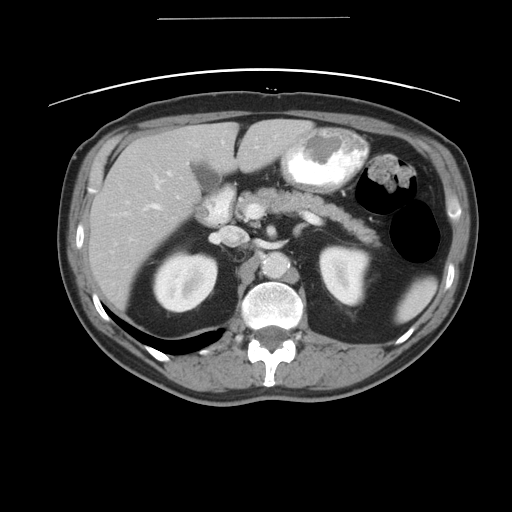
Contrast-enhanced abdominal CT, one axial slice. Position 25 of 49 along the scan axis. Reconstruction kernel STANDARD. 120 kVp. Intravenous contrast given. Soft-tissue window (W 400 / L 40 HU). 5 mm slice thickness. 512 × 512 image matrix, field of view 413 × 413 mm. Male patient, age 57 years. From the clinical record (not read from this slice): diagnosis: colorectal cancer liver metastases, imaged before liver resection; multiple liver metastases: yes; largest metastasis: 4 cm.
Outlined on this slice (manually delineated by an expert):
- hepatic veins: box from (x=110, y=170) to (x=165, y=251) px
- liver: (x=89, y=119)–(x=312, y=309)
- planned liver remnant (the part of the liver to remain after resection): (x=212, y=120)–(x=312, y=173)
- portal vein (with intrahepatic branches): (x=128, y=169)–(x=171, y=240)